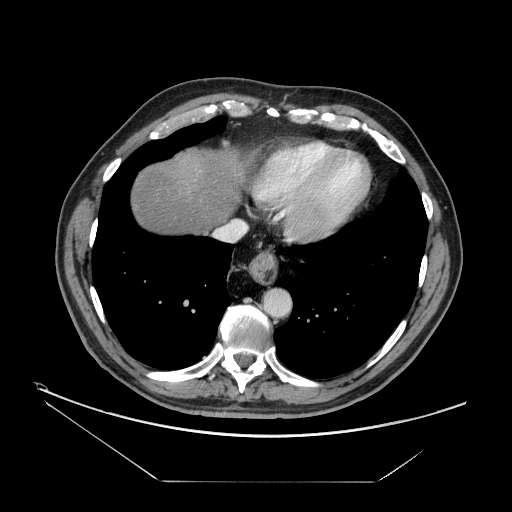
Contrast-enhanced abdominal CT, one axial slice; position 148 of 161 along the scan axis; reconstruction kernel STANDARD; 120 kVp; intravenous contrast given; soft-tissue window (W 400 / L 40 HU); 512 × 512 image matrix, field of view 440 × 440 mm. Male patient, age 65 years. Case-level facts recorded for this patient, not image findings: diagnosis: colorectal cancer liver metastases, imaged before liver resection; multiple liver metastases: yes; largest metastasis: 4.2 cm; disease in both lobes: yes.
Structures marked on this image (expert manual segmentation):
- hepatic veins: bounding box [x1, y1, x2, y2] px = [215, 190, 266, 241]
- liver: [130, 148, 243, 235]
- planned liver remnant (the part of the liver to remain after resection): [130, 148, 243, 235]